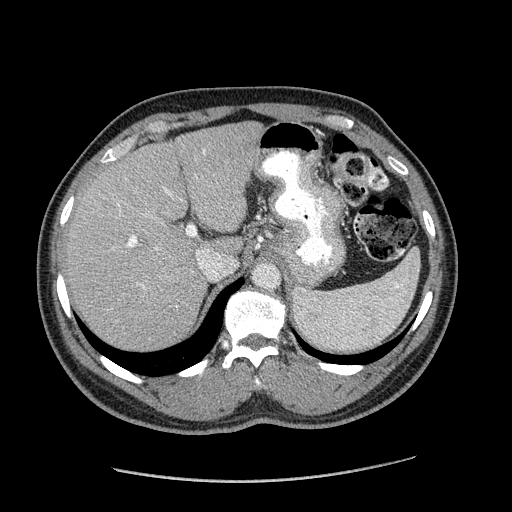
Contrast-enhanced abdominal CT (liver protocol), one axial slice; position 129 of 182 along the scan axis; soft-tissue window (W 400 / L 40 HU); 2.5 mm slice thickness; 512 × 512 image matrix, field of view 400 × 400 mm. From the clinical record (not read from this slice): diagnosis: hepatocellular carcinoma (patient treated with transarterial chemoembolisation; whether this scan precedes or follows treatment is not stated here); TNM stage (as recorded): Stage-I.
Annotated regions visible in this slice (semi-automatic segmentation, software-assisted and operator-edited):
- liver parenchyma outside the tumour (the mass and vessels are separate outlines, so this box may not span the whole liver): box from (x=64, y=122) to (x=262, y=350) px
- liver vessels: (x=117, y=149)–(x=206, y=288)